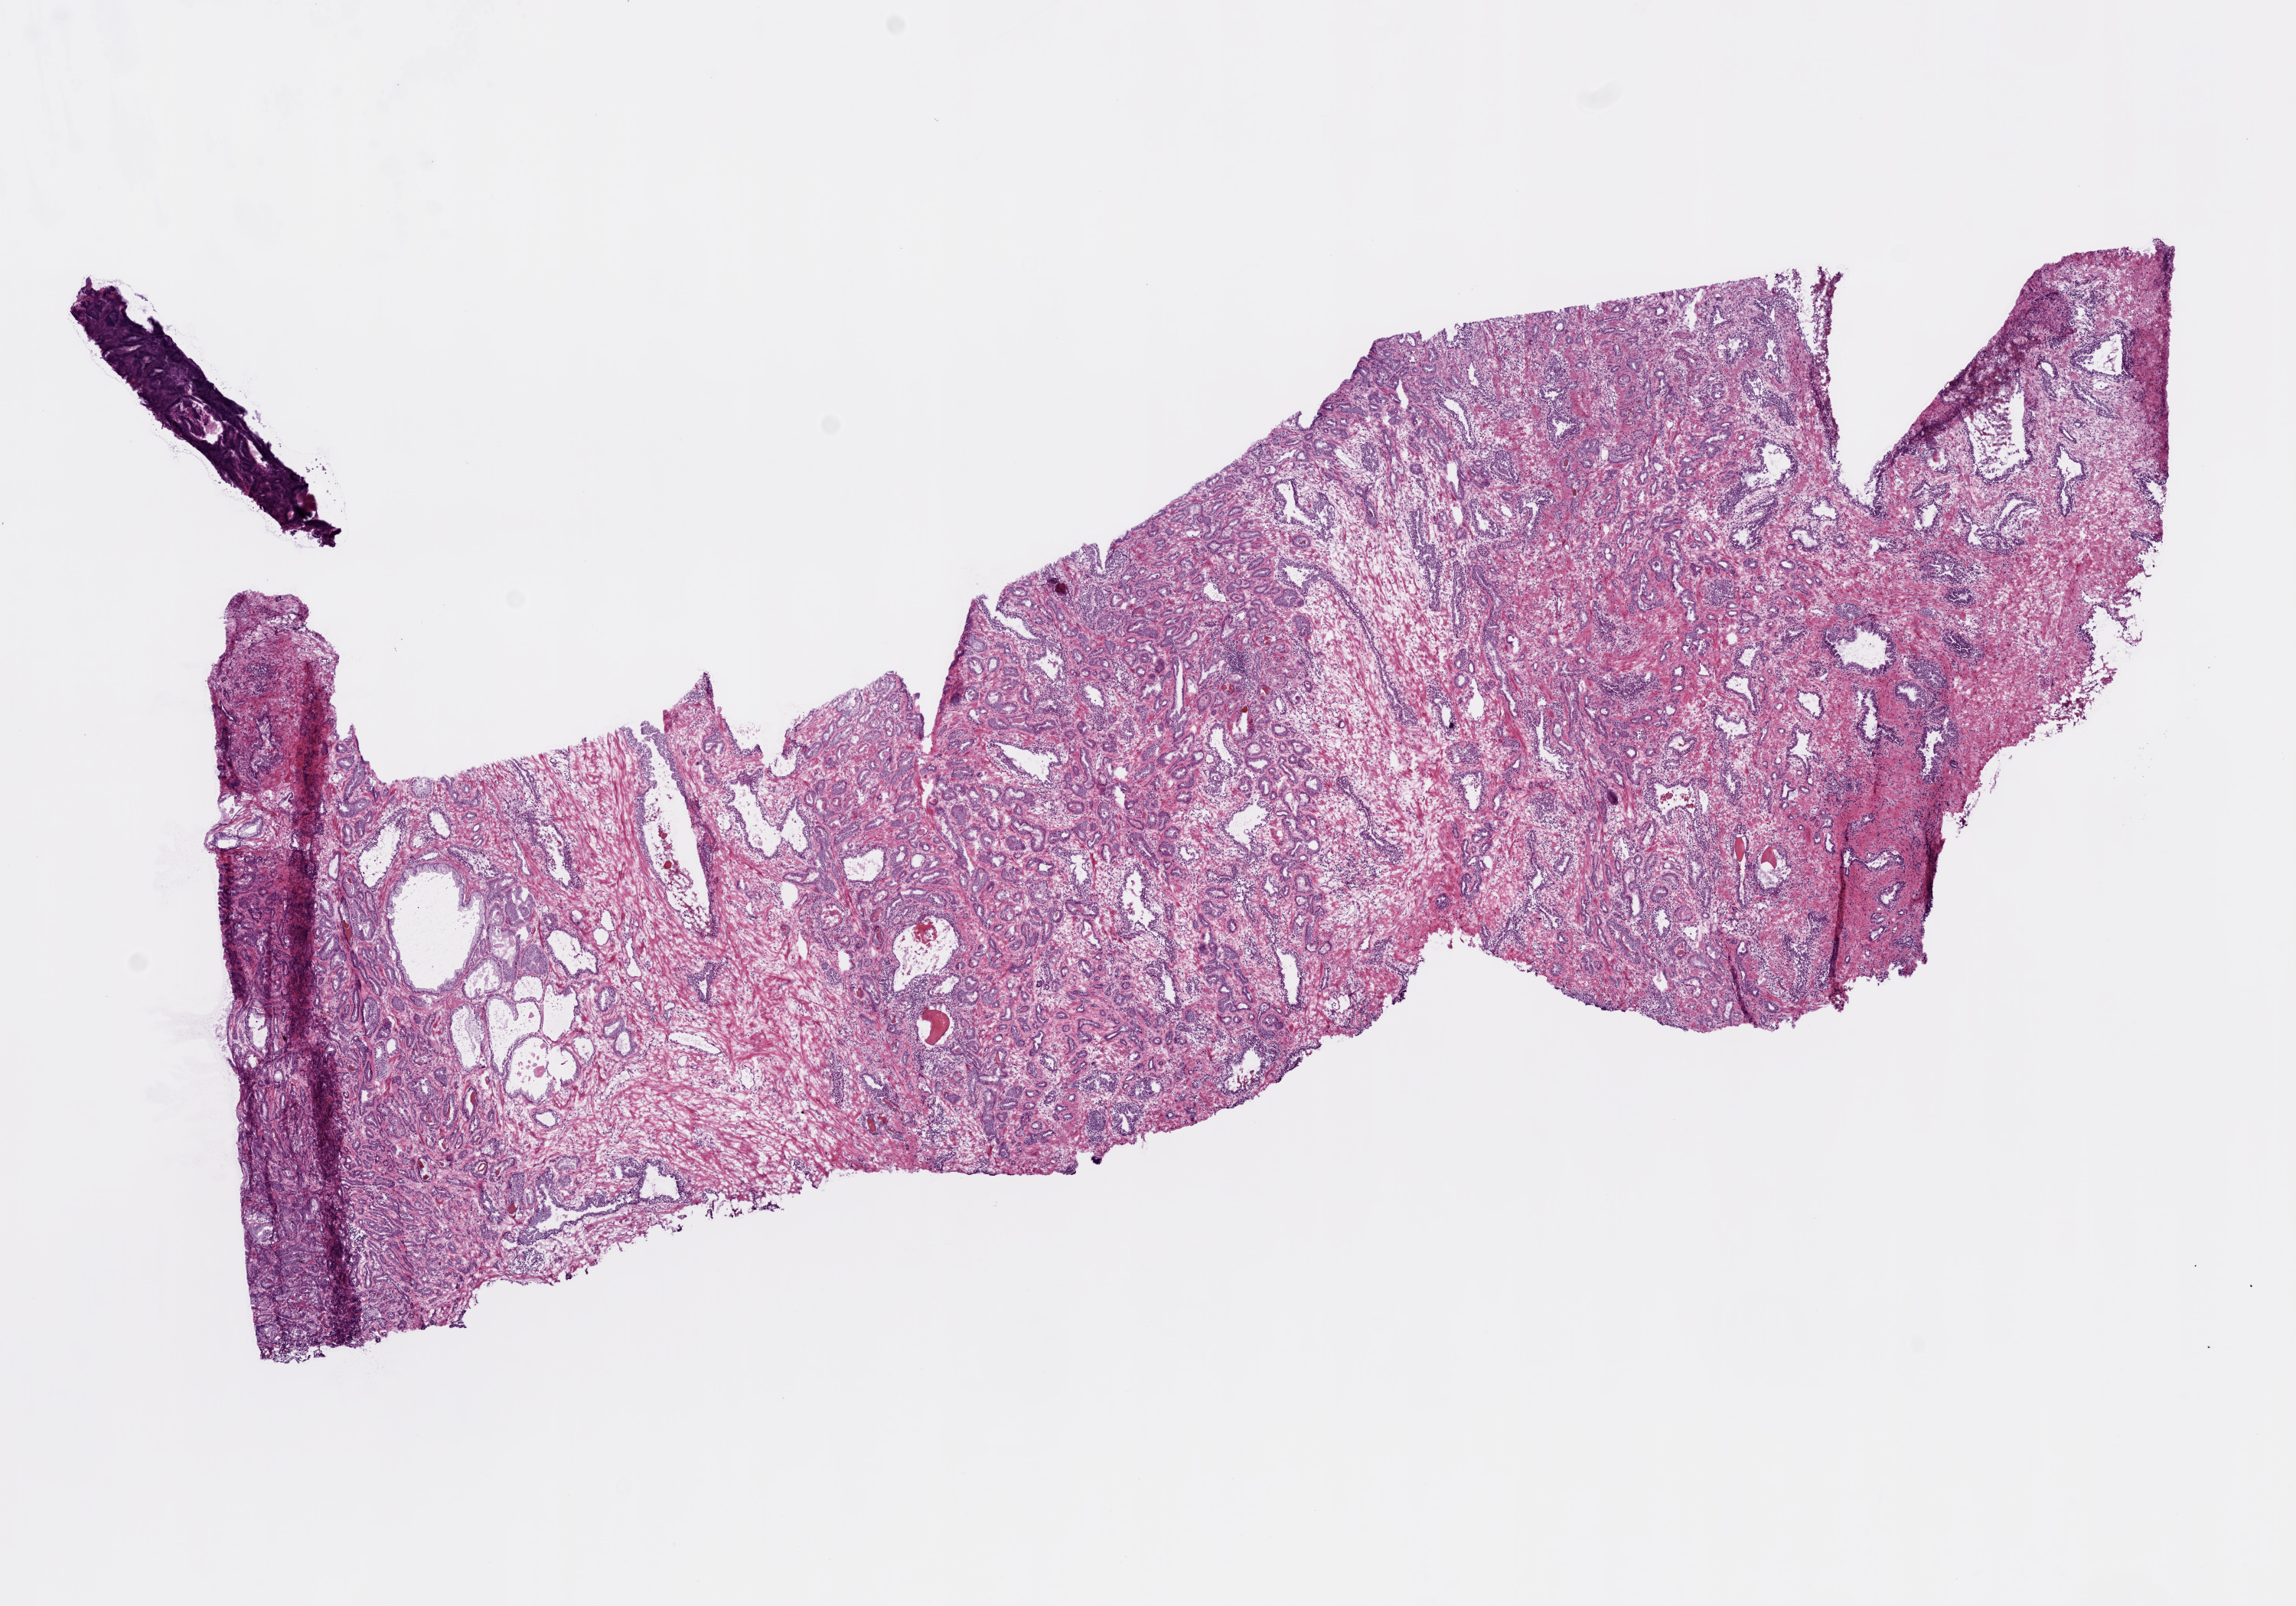
Whole-slide histology image, H&E-stained, shown as a low-resolution overview of the whole scanned area (about 12.0 x 8.4 mm). Frozen section from the bottom of the tissue portion. Sample: primary tumour, prostate. Patient: male, age at initial diagnosis 72 years. Gleason score: 6 (3+3). Slide review estimates, as recorded: tumour cells 60%, tumour nuclei 60%, normal cells 15%, stromal cells 25%, necrosis 0%. Inflammatory infiltration, as recorded: lymphocyte infiltration 0%, monocyte infiltration 0%, neutrophil infiltration 0%.
• histologic diagnosis: Acinar cell carcinoma (prostate gland)
• laterality: bilateral